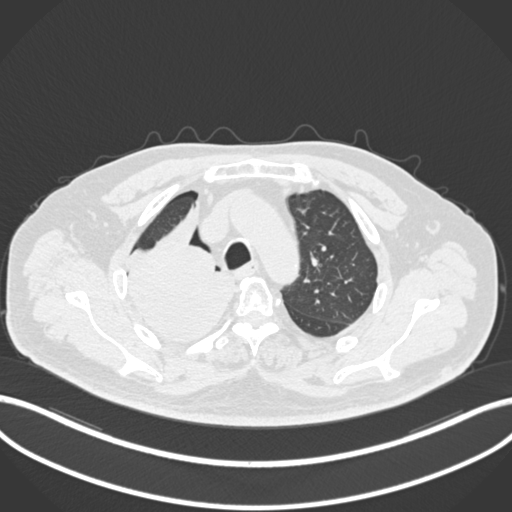
Chest CT, one axial slice; position 163 of 218 along the scan axis; reconstruction kernel B30f; lung window (W 1500 / L -600 HU); 1 mm slice thickness; 512 × 512 image matrix, field of view 400 × 400 mm. Male patient, age 68 years. From the clinical record (not read from this slice): clinical TNM (as recorded): T2a N0 M0.
Annotated regions visible in this slice (rectangle marked by the reading radiologist):
- lung tumour (recorded histology: adenocarcinoma): bounding box [x1, y1, x2, y2] px = [119, 200, 237, 343]